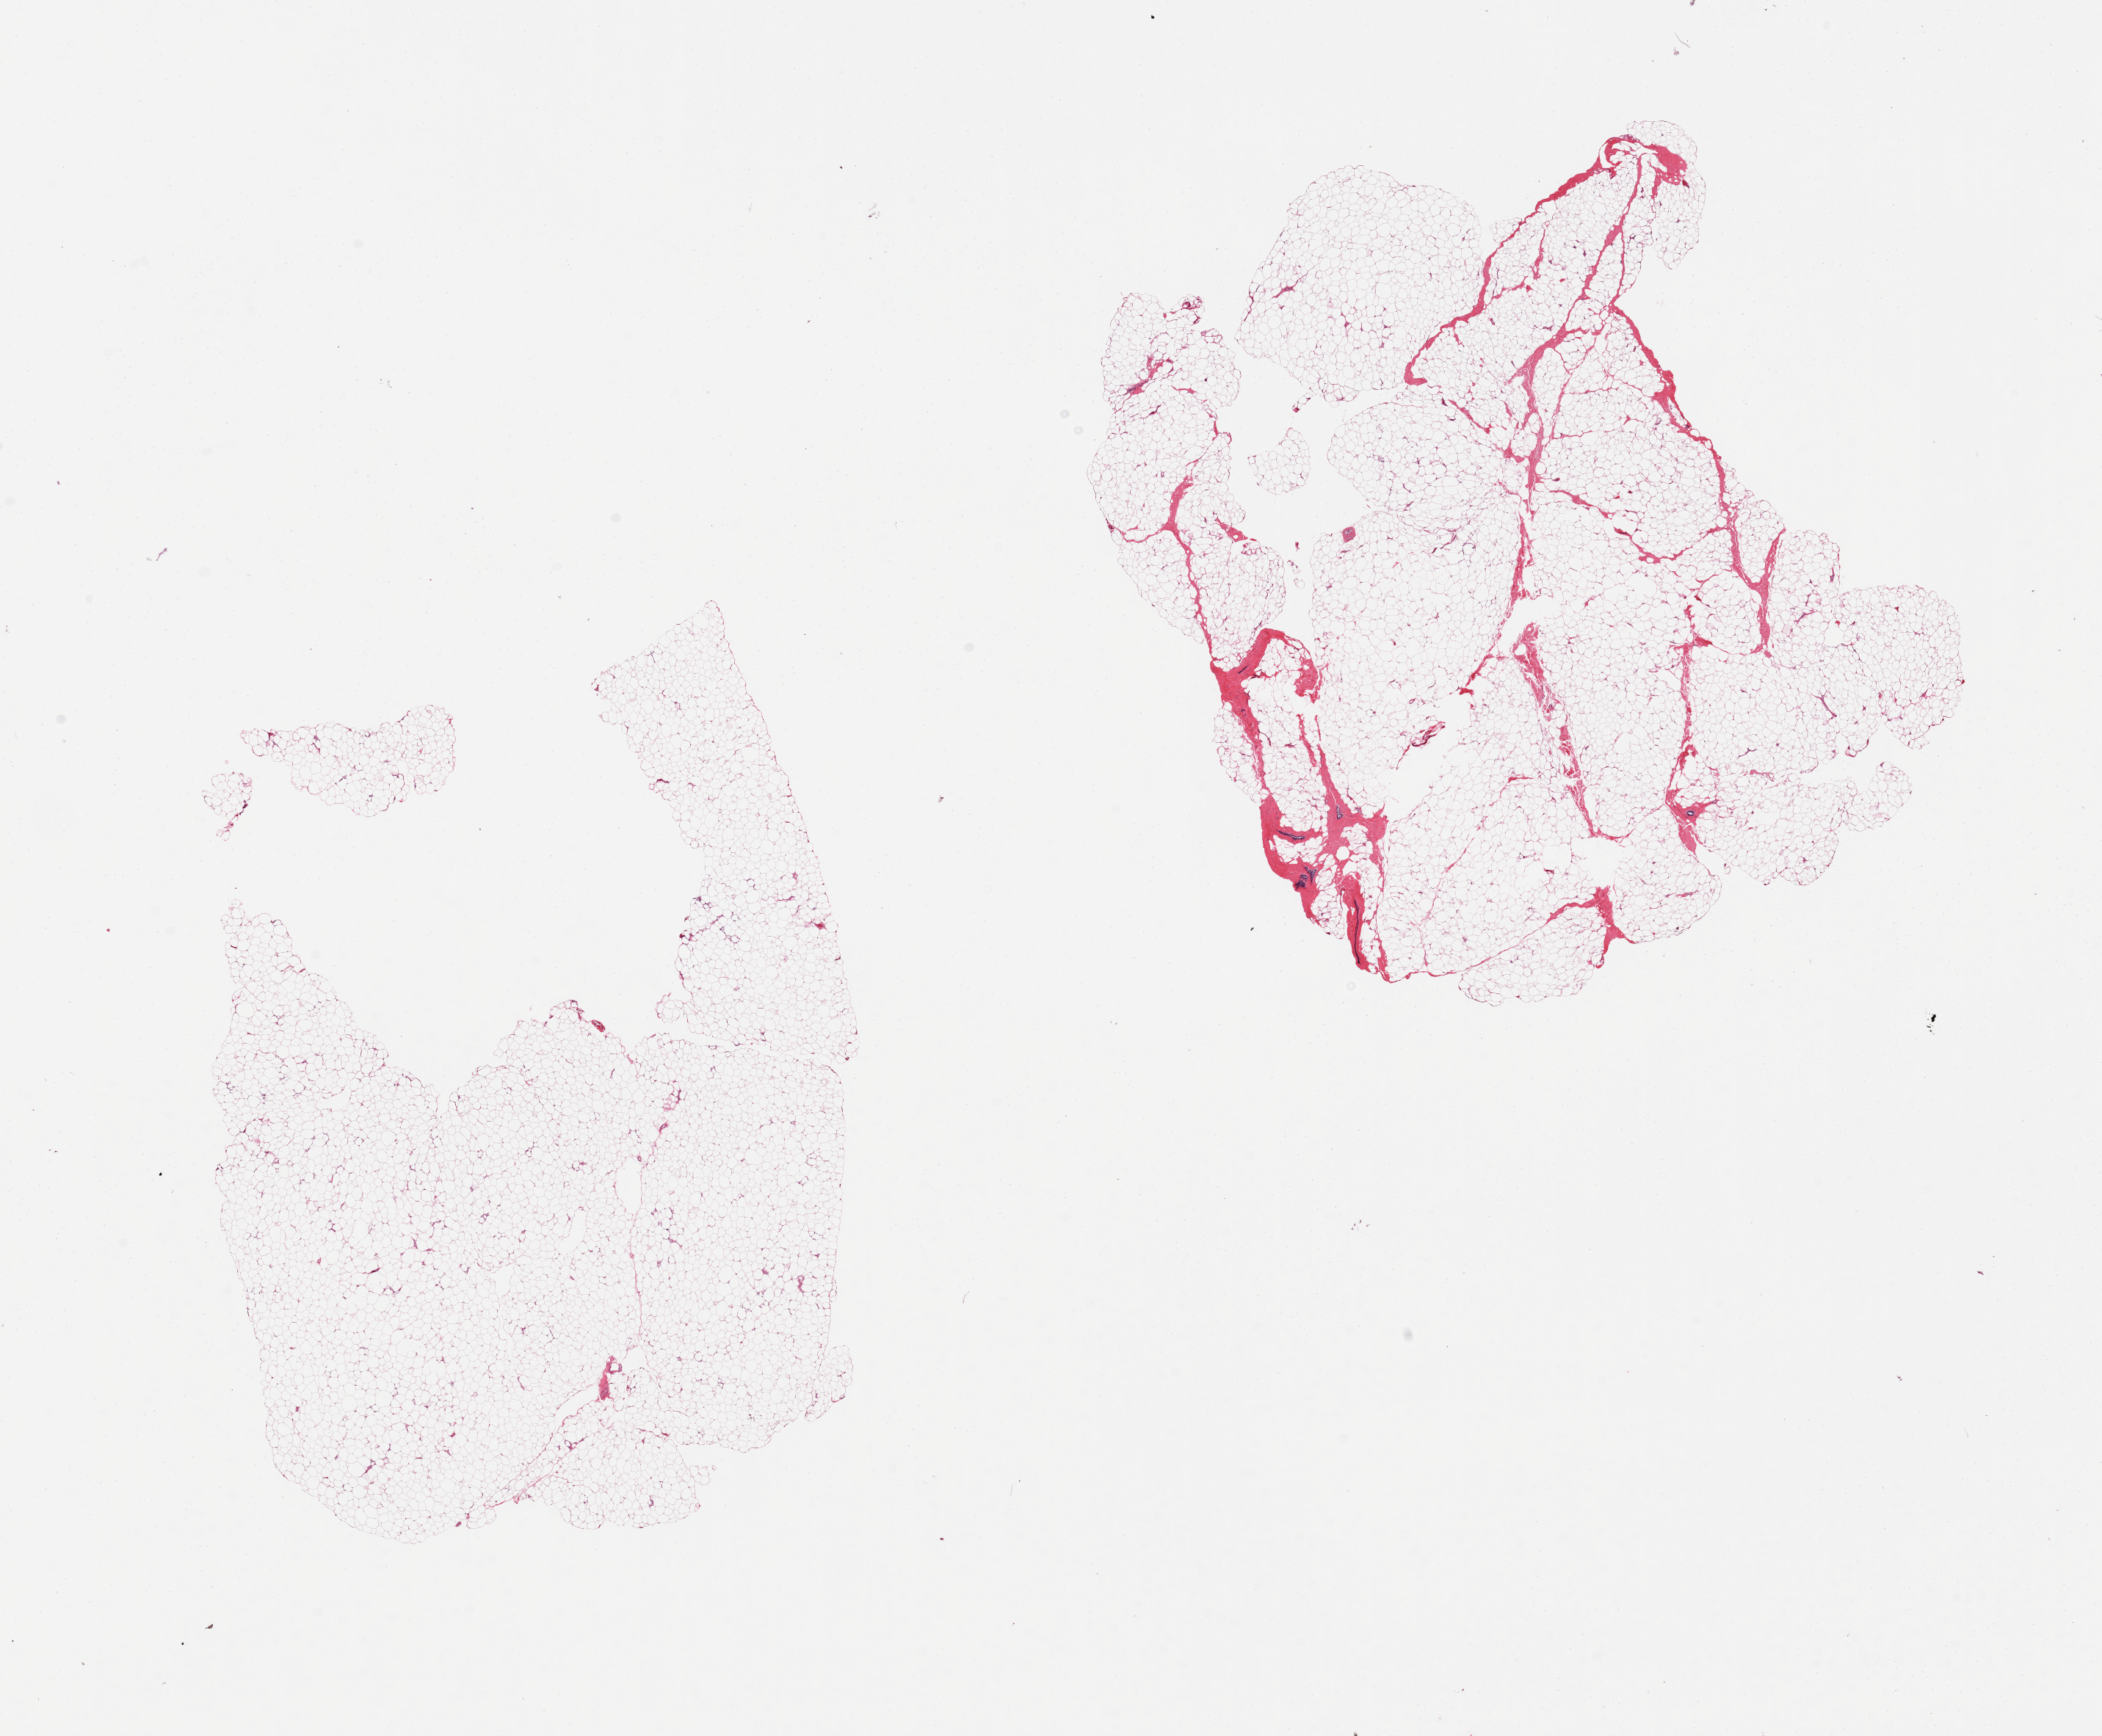
Digitized haematoxylin and eosin-stained section, low-resolution overview of the scanned area, about 22.6 x 18.7 mm. PAXgene-fixed paraffin-embedded (PFPE) section. Sampled site (target tissue): breast. Tissue donor sample. Donor: male.
Review note (as recorded): 2 pieces, fibroadipose, one aliquot with minute foci of ductal elements.